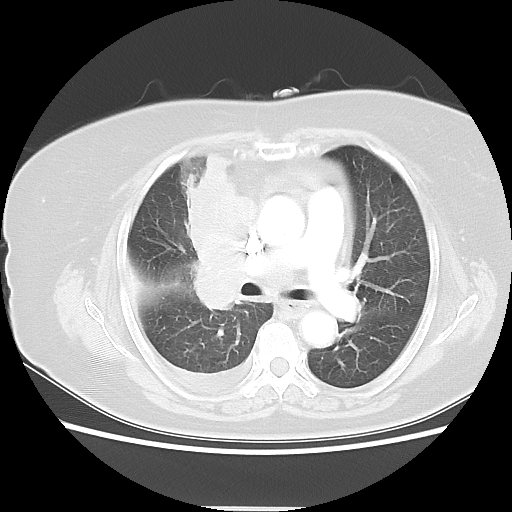
Chest CT, one axial slice. Slice 29 of 48 in the series (ordered by position). Lung window (W 1500 / L -600 HU). 5 mm slice thickness. 512 × 512 image matrix, field of view 360 × 360 mm. Female patient, age 73 years. Case-level facts recorded for this patient, not image findings: clinical TNM (as recorded): T3 N3 M1b; histopathological grade: G3.
Annotated regions visible in this slice (rectangle marked by the reading radiologist):
- lung tumour (recorded histology: small cell carcinoma): bounding box <181,149,261,317> (left, top, right, bottom; pixels)